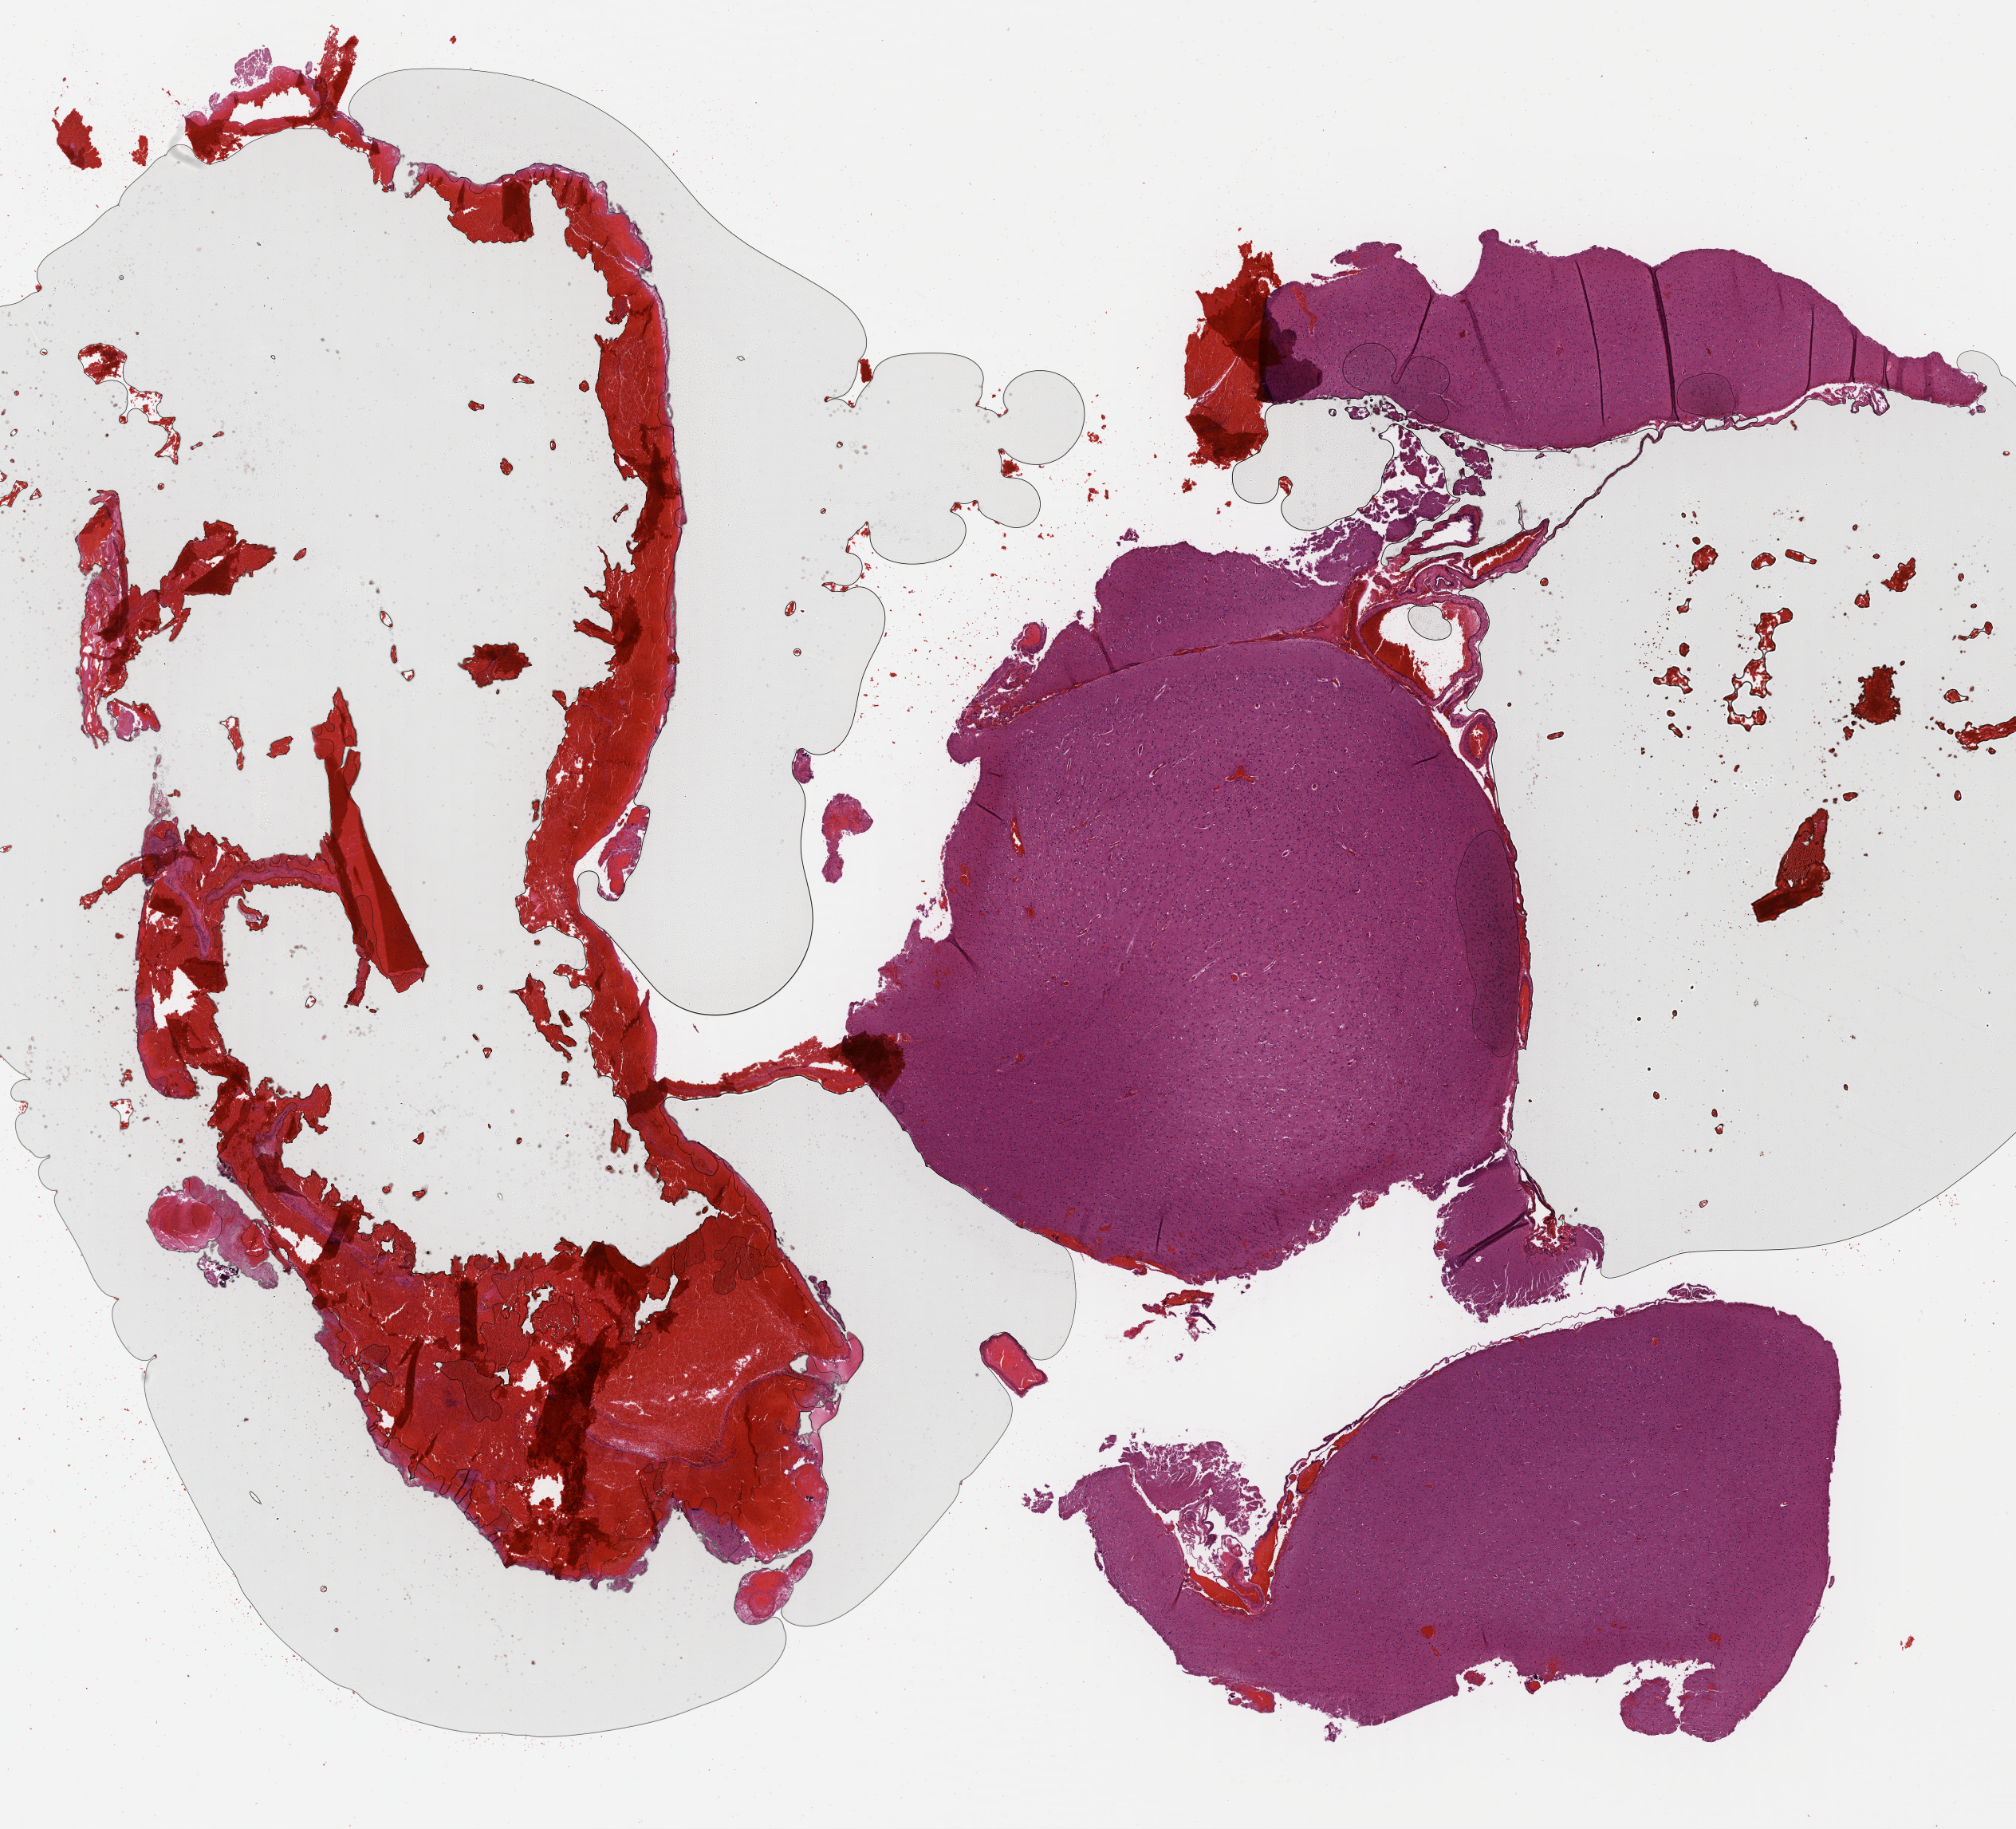
H&E-stained whole-slide image, whole scanned area (about 19.9 x 18.0 mm) shown as a low-resolution overview; formalin-fixed paraffin-embedded (FFPE) diagnostic section; brain, primary tumour sample. Female, age 61 years at initial diagnosis. Histologic grade: G2 (moderately differentiated).
* laterality: left
* histologic diagnosis: Astrocytoma, NOS (cerebrum)